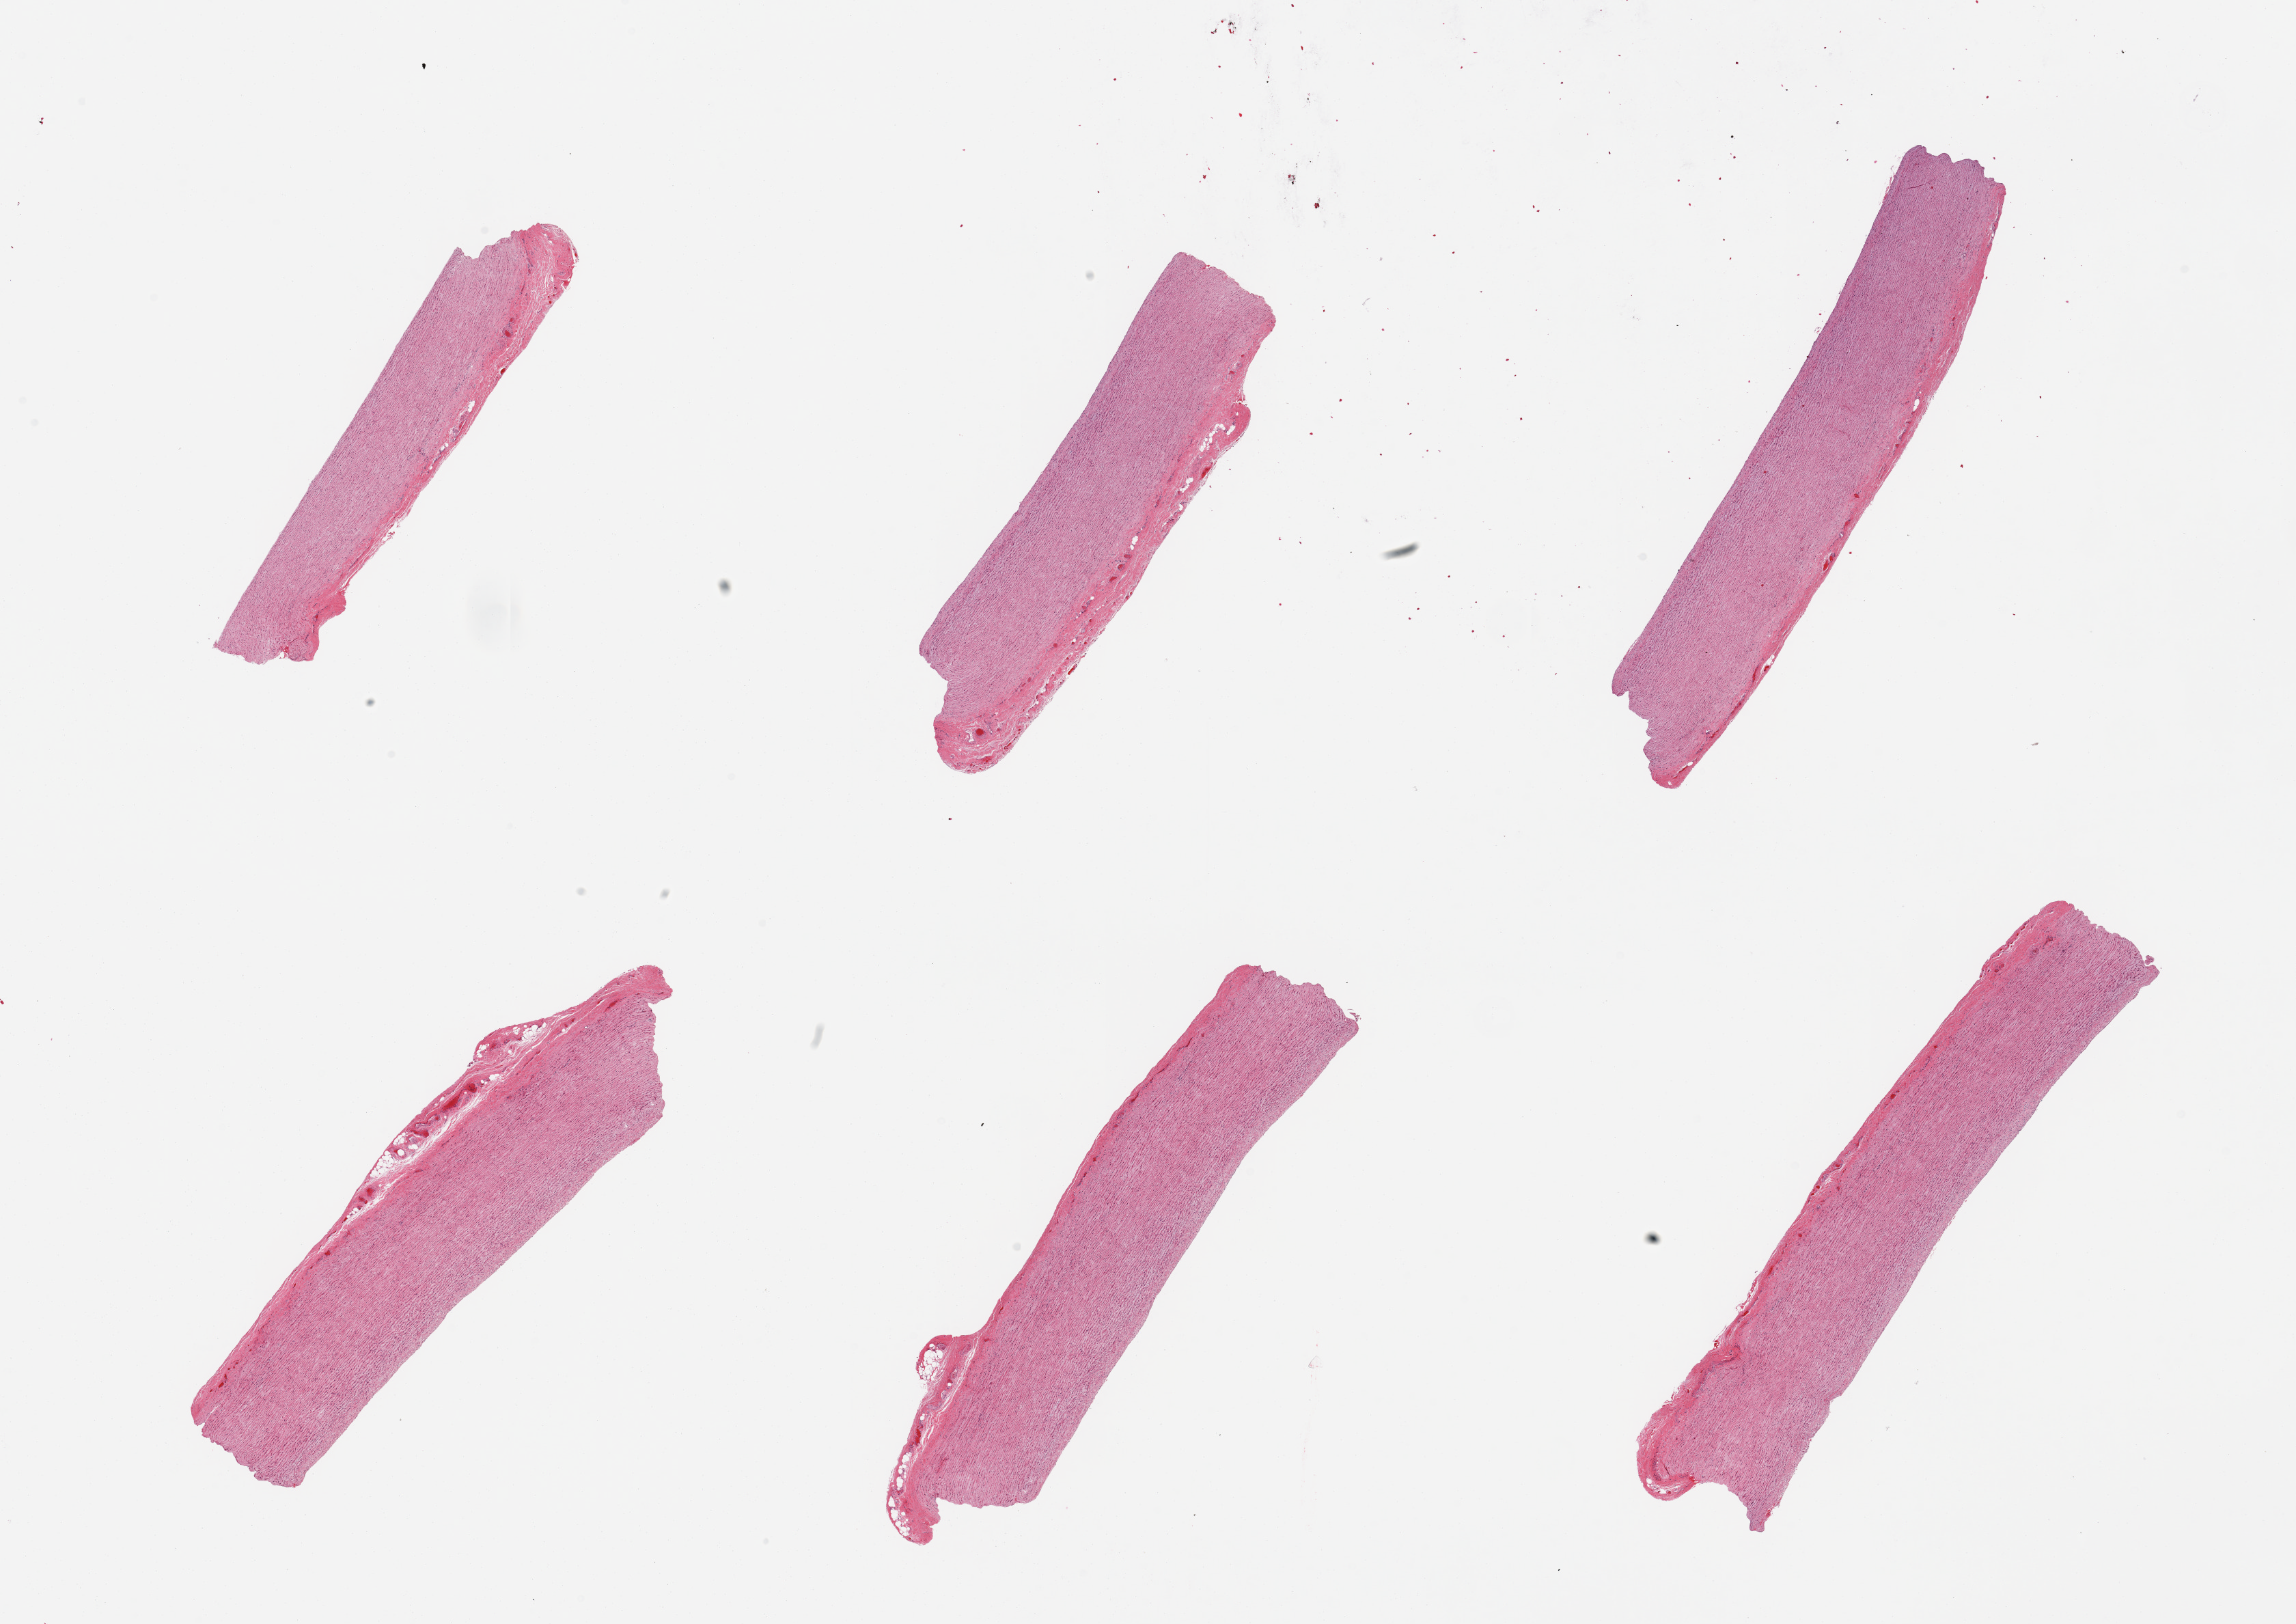
Whole-slide image, H&E stain, brightfield, a low-resolution overview of the entire scanned area, about 26.6 x 18.8 mm. PAXgene-fixed paraffin-embedded (PFPE) section. Section of aorta (target tissue). Donor tissue sample. Donor: male.
Pathologist's review note for this sample: 6 pieces, no significant atherosis noted.